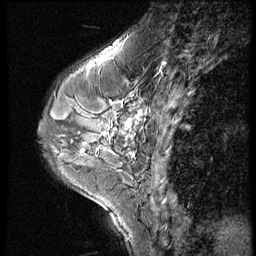
Breast MRI (dynamic contrast-enhanced), one sagittal slice. Slice 22 of 56 in the series (ordered by position). 3 images stored at this slice position (order not interpretable as contrast timing). 1.5 T. TE 4.2 ms, TR 9 ms. 2.5 mm slice thickness. 256 × 256 image matrix, field of view 180 × 180 mm. Patient: female, 46 years. Case-level facts recorded for this patient, not image findings: setting: breast cancer imaged before/during neoadjuvant chemotherapy; receptor status: HER2-positive.
Structures marked on this image (semi-automatic segmentation, software-assisted and operator-edited):
- analysis volume of interest (the breast-tissue region the enhancement analysis was run in; not a lesion): bounding box <73,86,164,161> (left, top, right, bottom; pixels)
- tumour enhancement mask (voxels above the 140 % enhancement threshold inside the analysis volume of interest): <83,112,140,156>